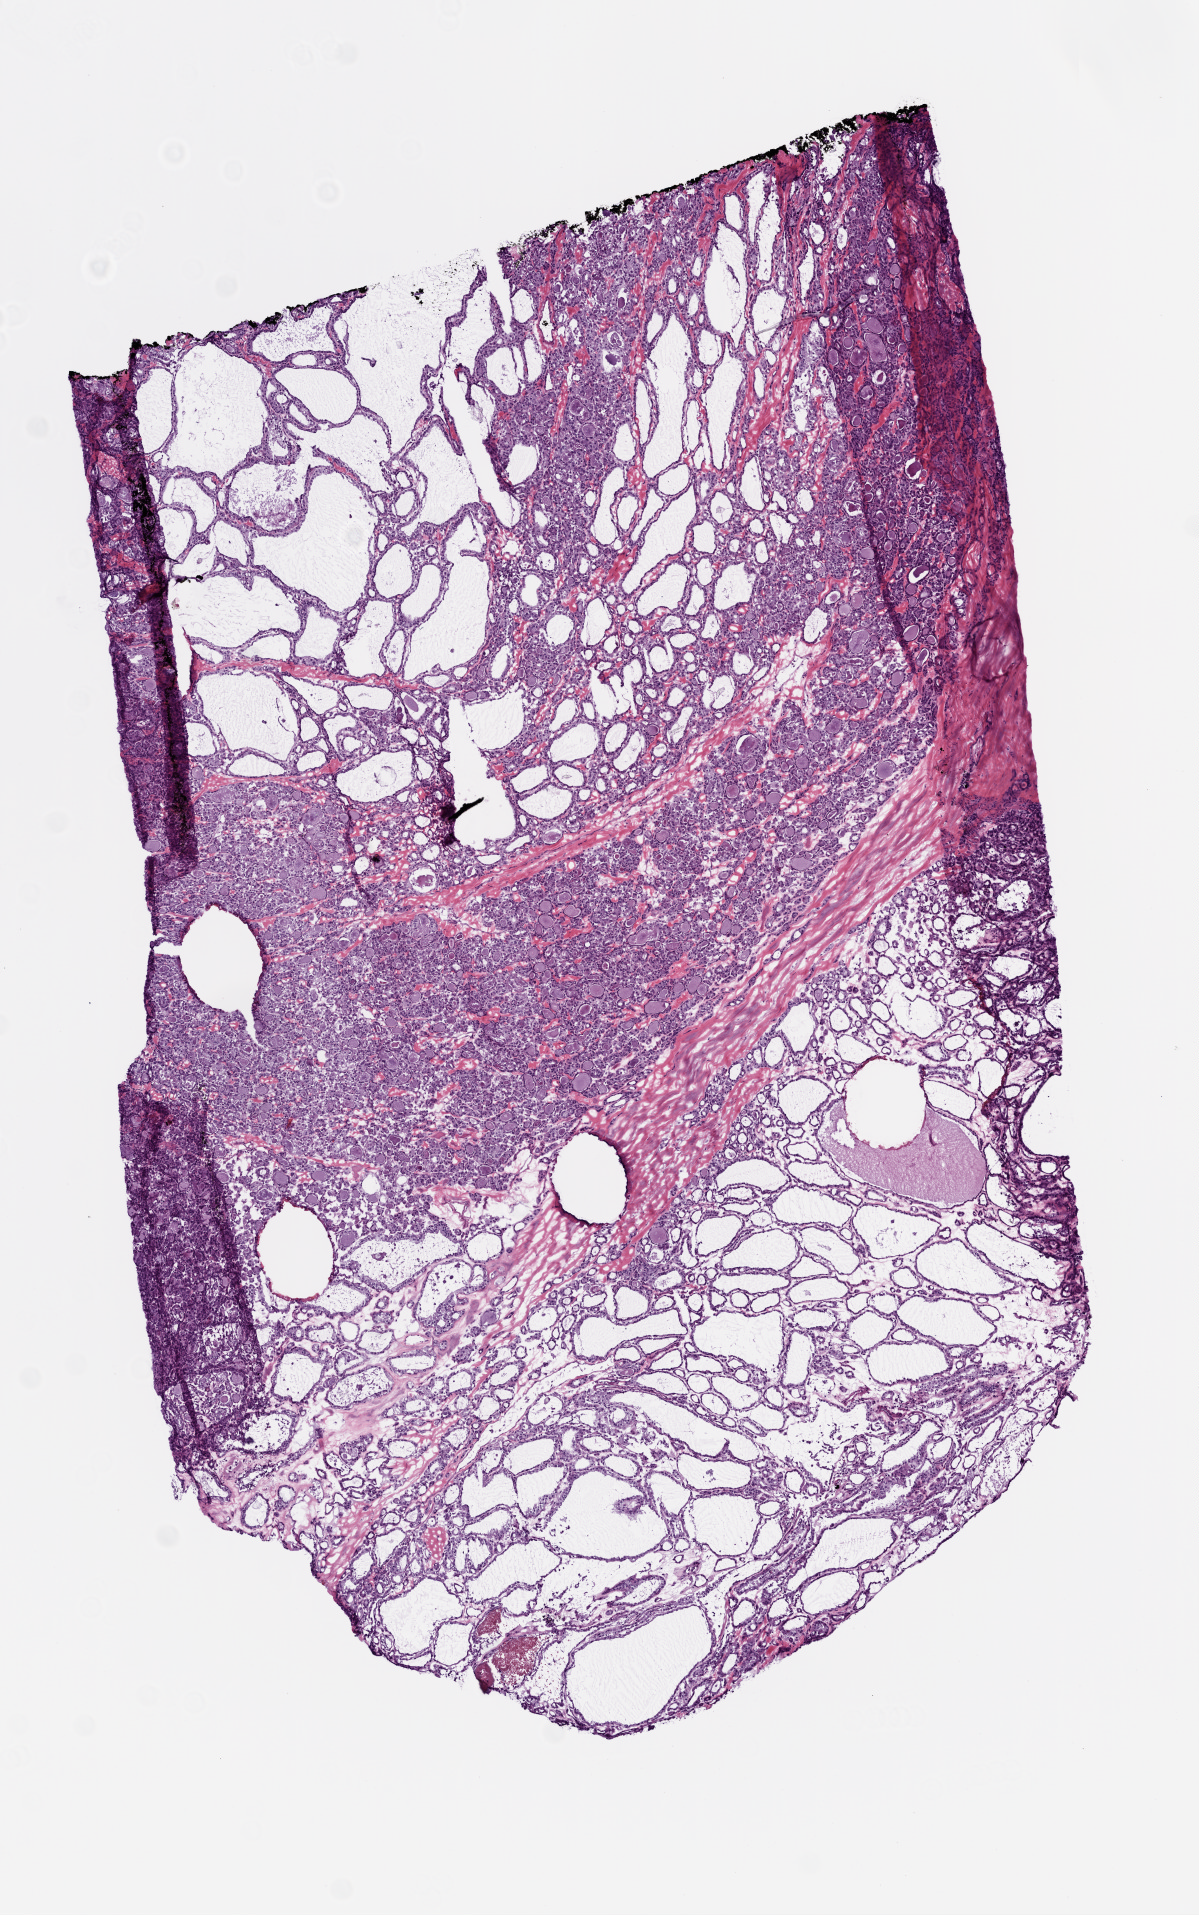
Digitized H&E-stained tissue section (whole slide) — low-resolution overview of the scanned area, about 4.8 x 7.7 mm, frozen section from the top of the tissue portion, thyroid, primary tumour sample. Patient: male, age at initial diagnosis 69 years. Pathologist review of this section (percent, as recorded): tumour cells 95%, tumour nuclei 85%, normal cells 5%, stromal cells 0%, necrosis 0%. Infiltration values recorded for this section: lymphocyte infiltration 0%, monocyte infiltration 0%, neutrophil infiltration 0%.
* TNM: T1 N0 M0
* laterality: right
* histologic diagnosis: Papillary carcinoma, follicular variant (thyroid gland)
* AJCC pathologic stage: I (7th edition)